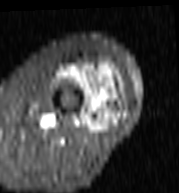
MRI of an extremity soft-tissue mass, one axial slice. Position 39 of 103 along the scan axis. STIR. MR volume resampled by the dataset authors to the PET/CT grid (not the native acquisition matrix). 3.27 mm slice thickness. 179 × 193 image matrix. Female patient. From the clinical record (not read from this slice): histological type: undifferentiated – high grade; grade: high; site of the primary tumour: left thigh.
Annotated regions visible in this slice (expert contour drawn on MRI and transferred to this co-registered scan by the dataset authors):
- gross tumour volume including surrounding oedema: bounding box [x1, y1, x2, y2] px = [59, 60, 124, 132]
- gross tumour volume (mass): [93, 71, 119, 132]